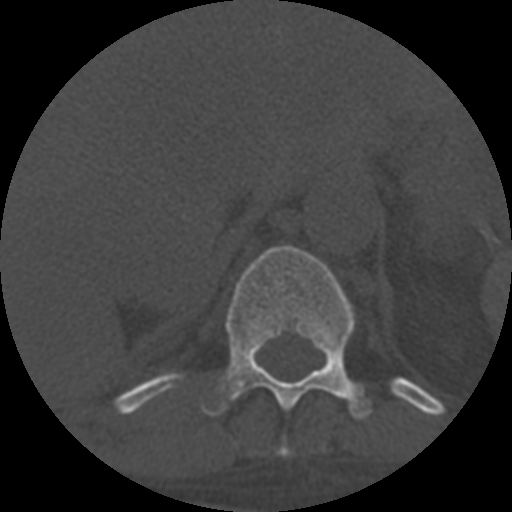
CT including the spine, one axial slice. Slice 337 of 708 in the series (ordered by position). One of 3 acquisitions stored at this slice position. Bone window (W 1800 / L 400 HU). 512 × 512 image matrix. Patient age 55 years. Case-level facts recorded for this patient, not image findings: primary cancer: colon; vertebrae with lytic lesions (as recorded): T12, L1, L5.
Annotated regions visible in this slice (semi-automatic segmentation, software-assisted and operator-edited):
- T10 vertebra: bounding box <278,443,290,457> (left, top, right, bottom; pixels)
- T11 vertebra: <201,245,371,420>